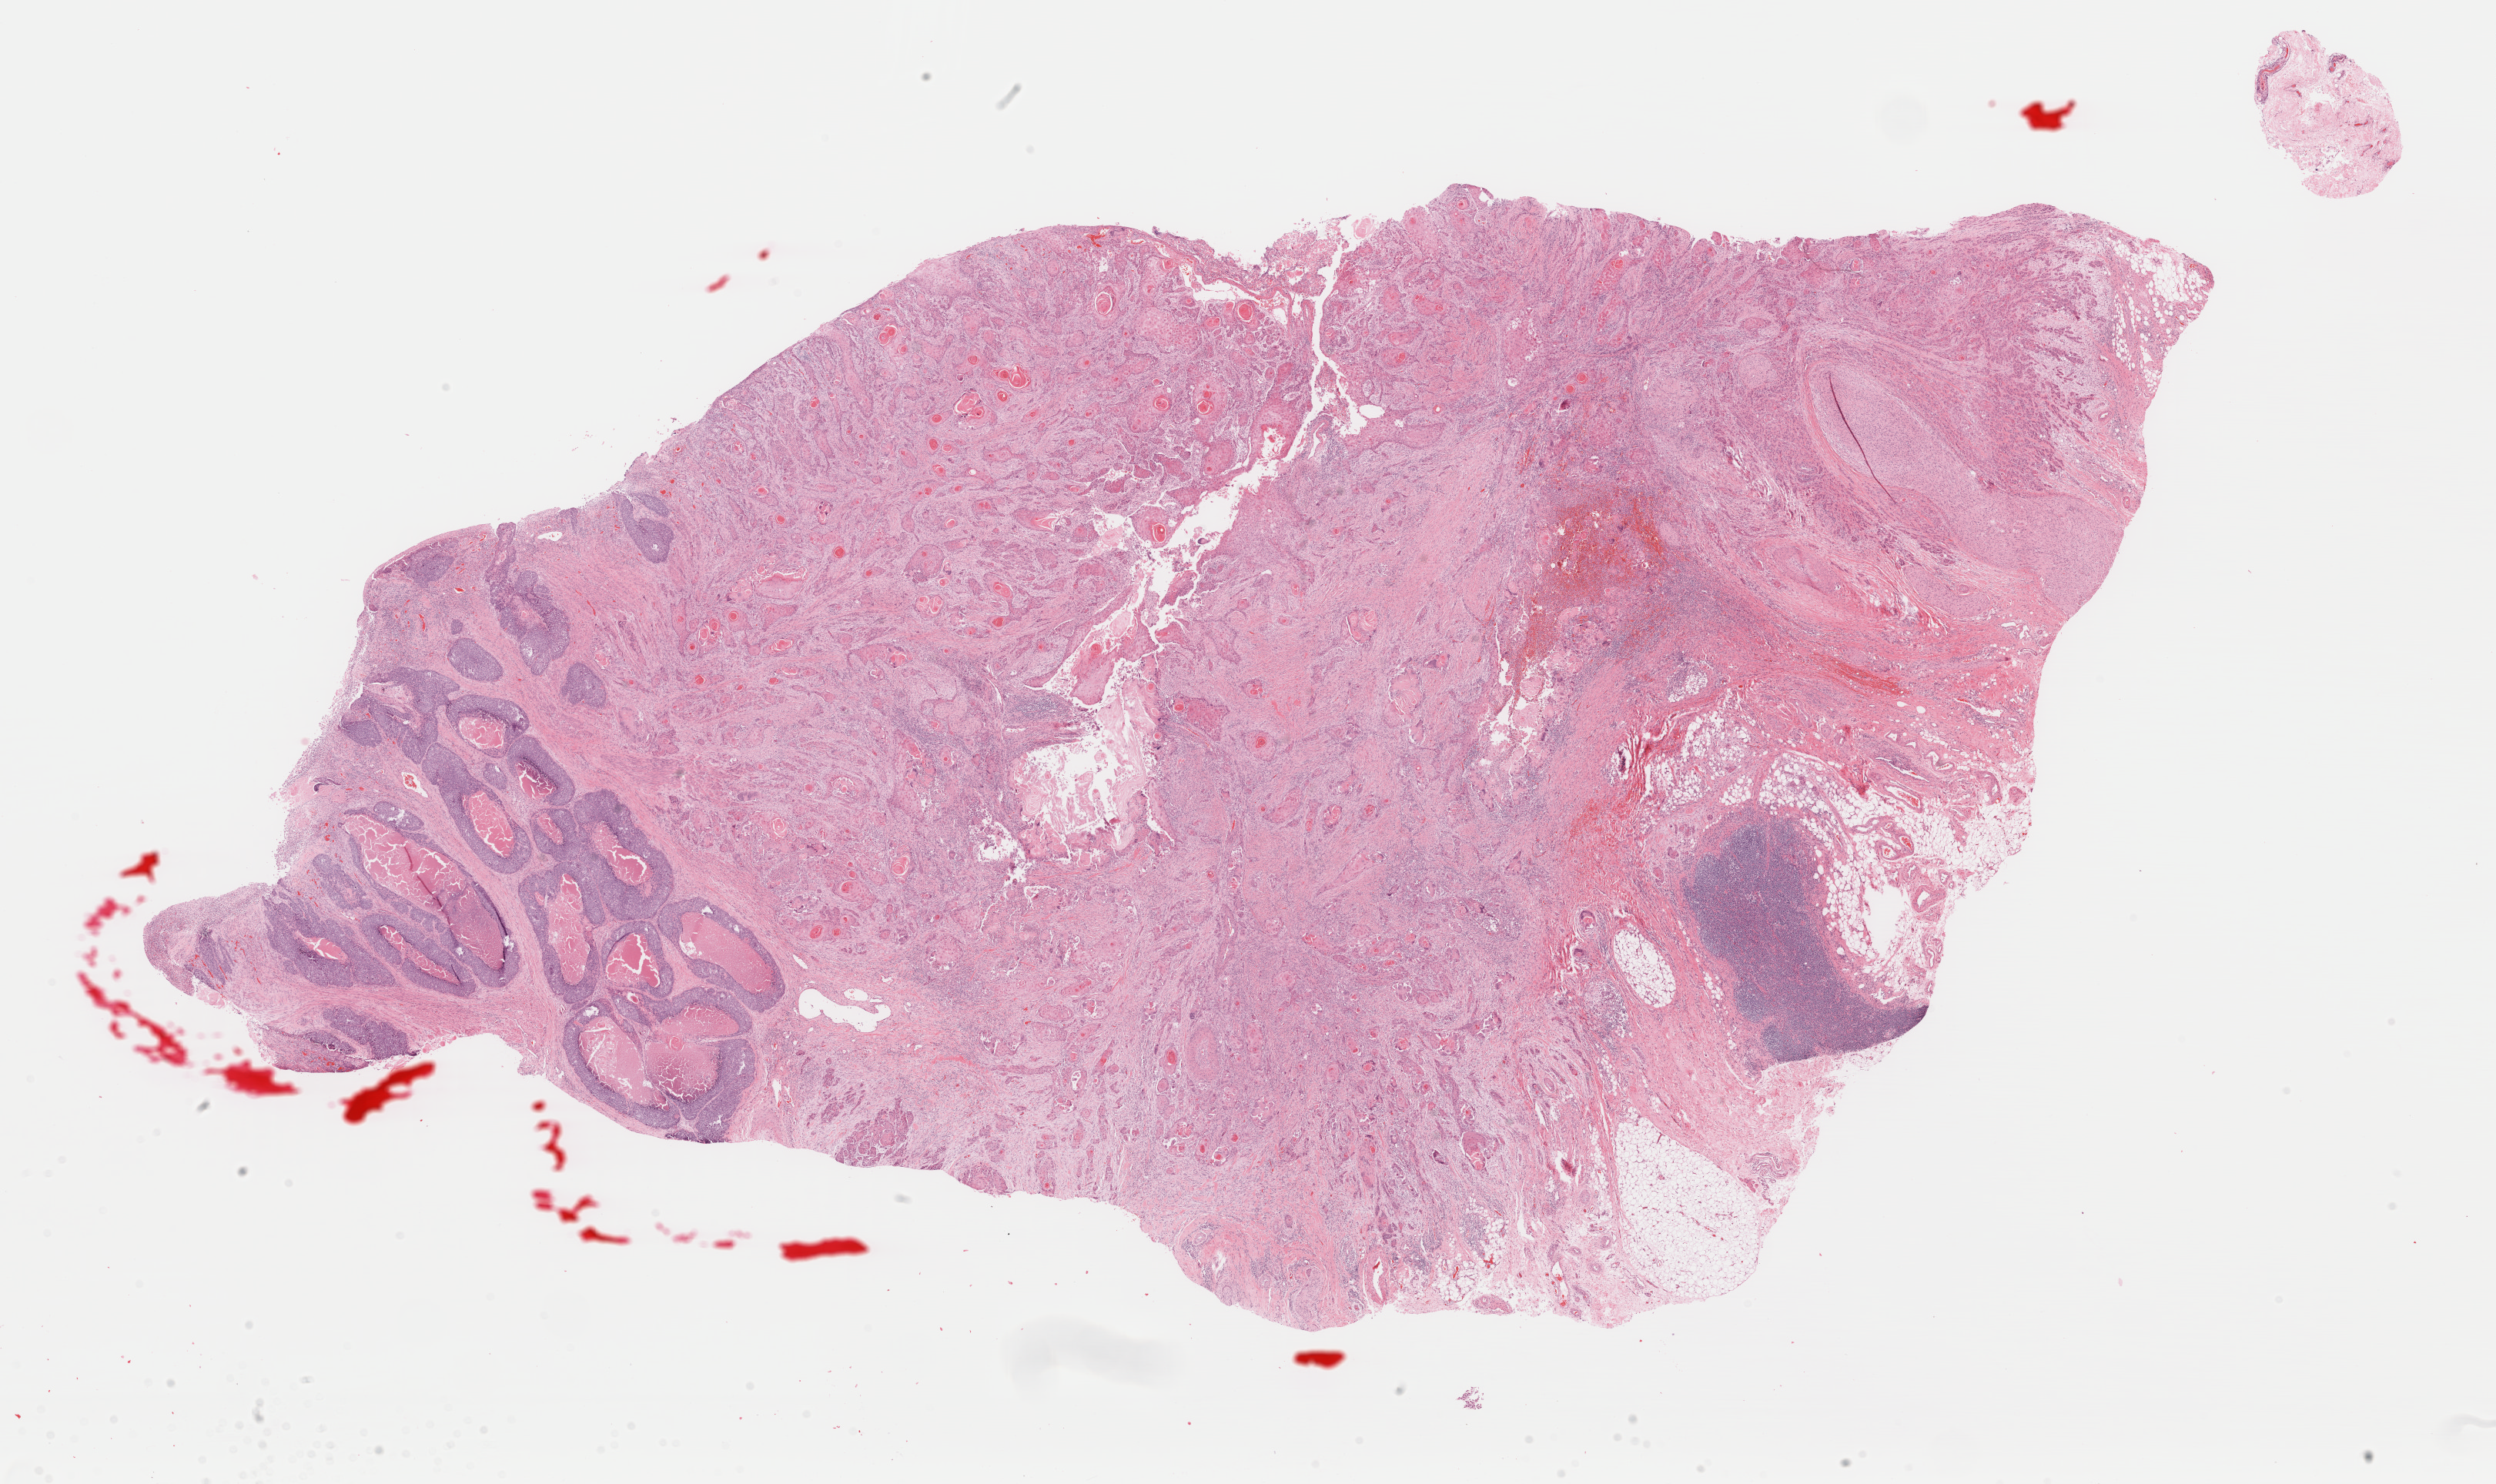
Digitized H&E-stained tissue section (whole slide), shown as a low-resolution overview of the whole scanned area (about 25.6 x 15.2 mm, acquisition: 40x scan). FFPE section. Sample: primary tumour, esophagus. Patient: male, age at initial diagnosis 72 years. Histologic grade: G2 (moderately differentiated).
AJCC pathologic stage: IIIA (7th edition). Lymph nodes positive (case pathology): 0 of 12 examined. Histologic diagnosis: Squamous cell carcinoma, NOS.